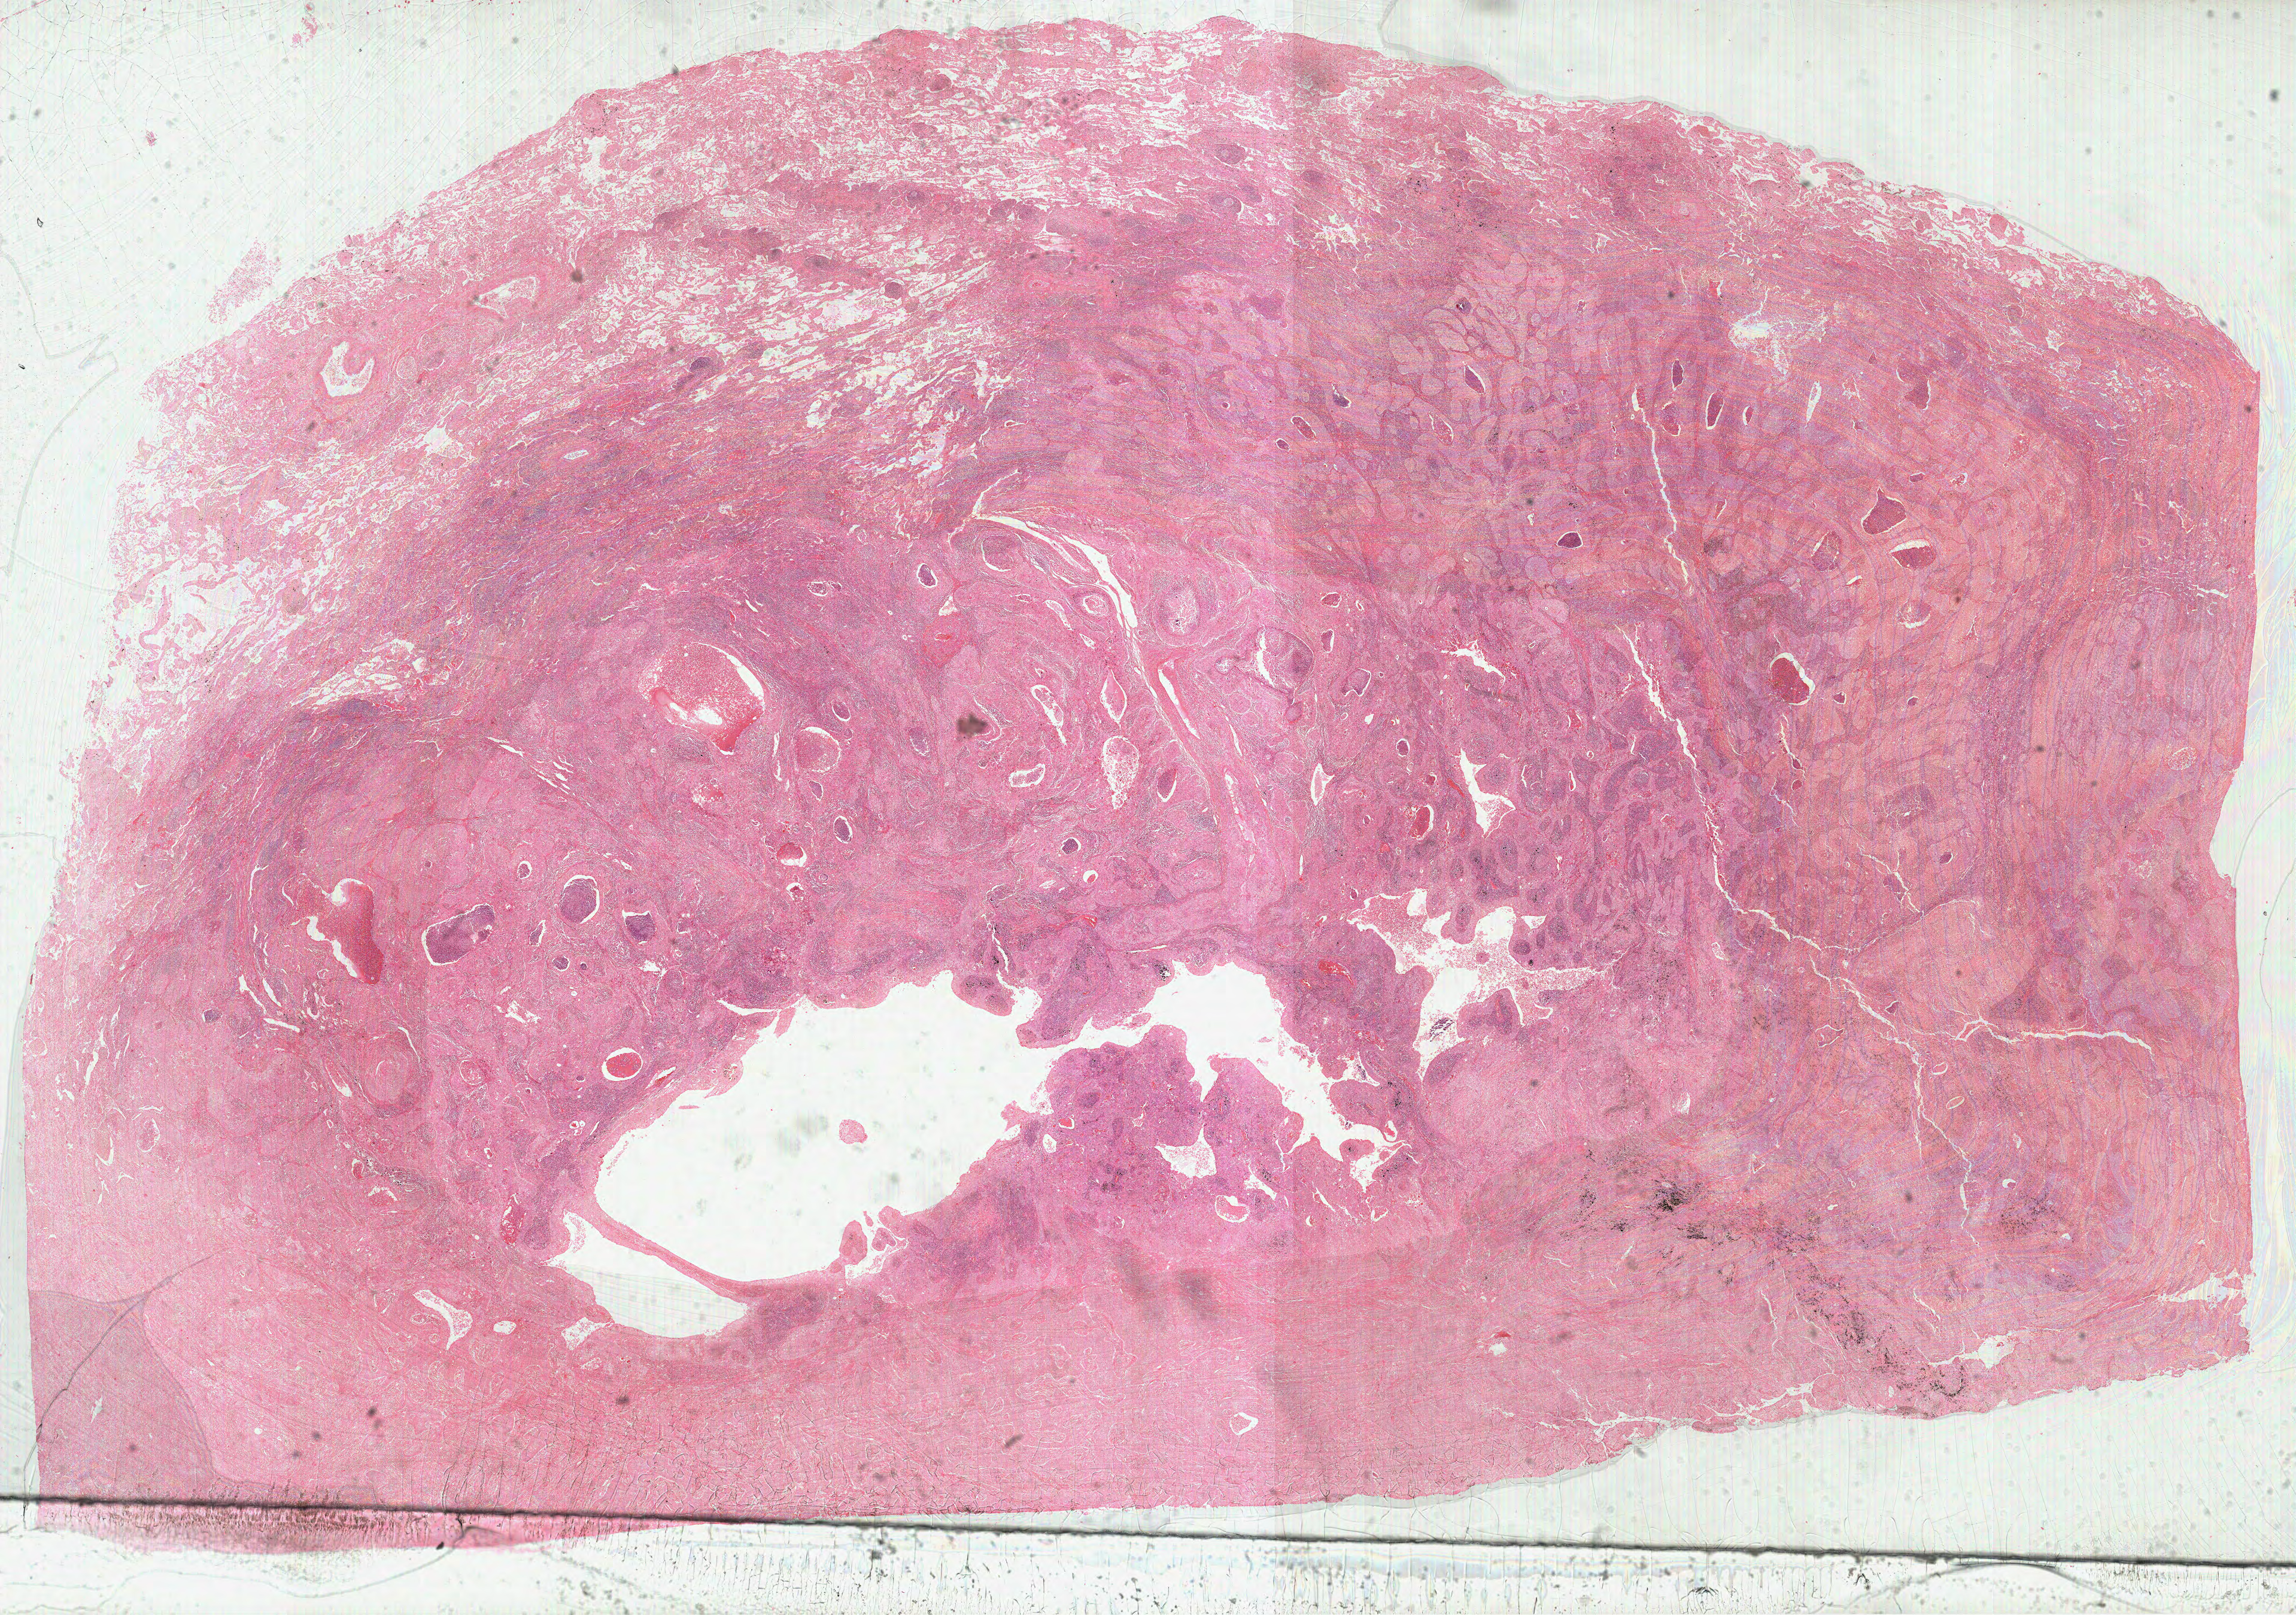
Digitized Hematoxylin and eosin (H&E) stained tissue section (whole slide) — shown as a low-resolution overview of the whole scanned area (about 30.9 x 21.8 mm, acquisition: 40x scan). FFPE section. Lung, primary tumour sample. Patient: male, age at initial diagnosis 72 years.
AJCC pathologic stage: IIB (6th edition). Histologic diagnosis: Squamous cell carcinoma, NOS (upper lobe, lung).